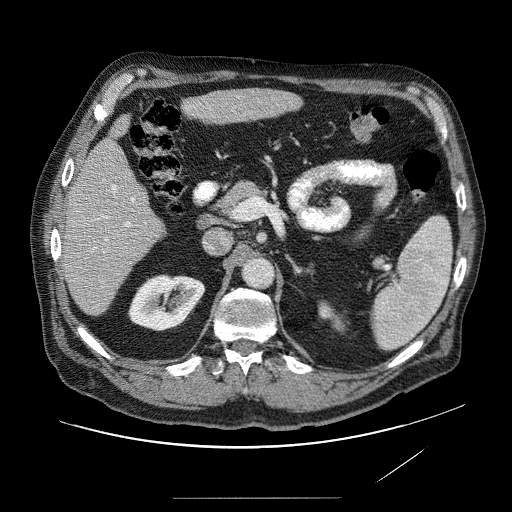
Contrast-enhanced abdominal CT (liver protocol), one axial slice. Slice 34 of 89 in the series (ordered by position). Reconstruction kernel STANDARD. 120 kVp. Soft-tissue window (W 400 / L 40 HU). 512 × 512 image matrix, field of view 420 × 420 mm. Case-level facts recorded for this patient, not image findings: diagnosis: hepatocellular carcinoma (patient treated with transarterial chemoembolisation; whether this scan precedes or follows treatment is not stated here); TNM stage (as recorded): Stage-IVA; Child-Pugh class: A; tumour differentiation: moderately differentiated; tumour nodularity: multinodular.
Annotated regions visible in this slice (semi-automatically segmented with operator editing):
- liver parenchyma outside the tumour (the mass and vessels are separate outlines, so this box may not span the whole liver): bounding box (x1, y1, x2, y2) in pixels: (62, 86, 306, 318)
- mass: (183, 95, 207, 123)
- liver vessels: (89, 109, 237, 296)